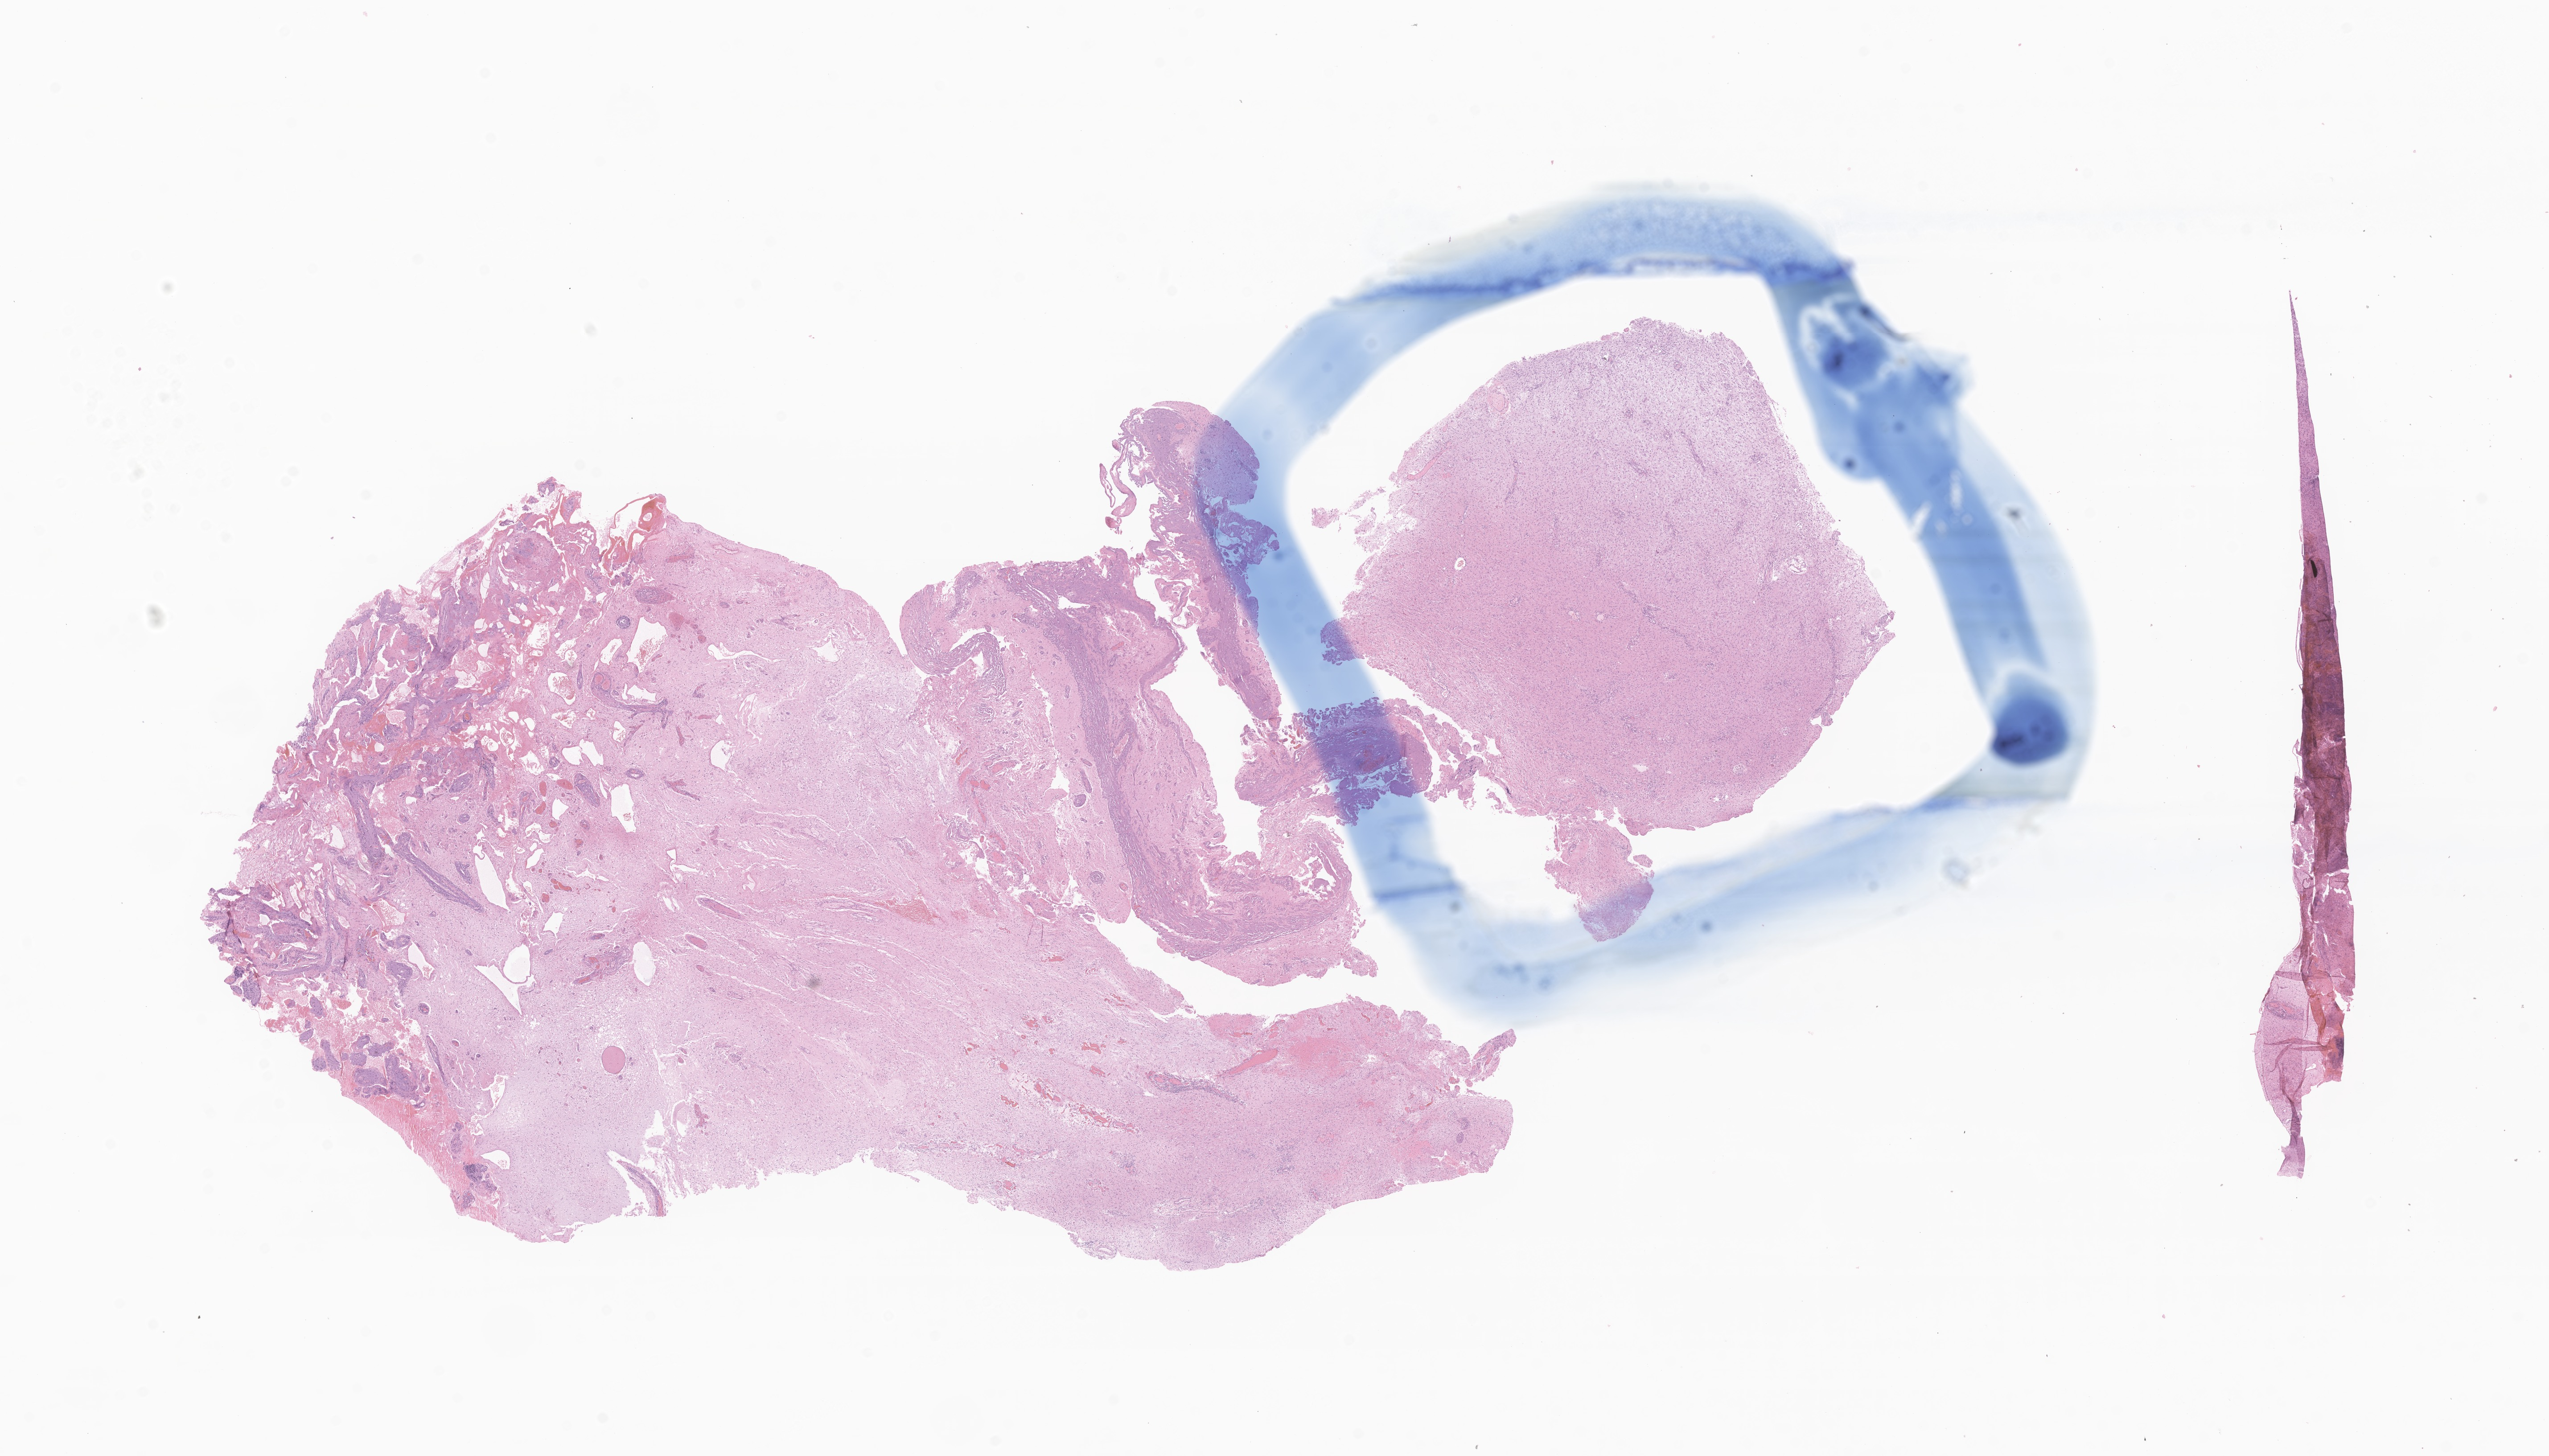
Whole-slide image, hematoxylin and eosin (H&E) stain of tumor tissue from the brain, shown as a low-resolution overview of the whole scanned area (about 24.1 x 13.8 mm), formalin-fixed, paraffin-embedded (FFPE) tissue. Male patient, age 141 months.
- diagnosis (ICD-O-3 morphology term): Pilocytic astrocytoma